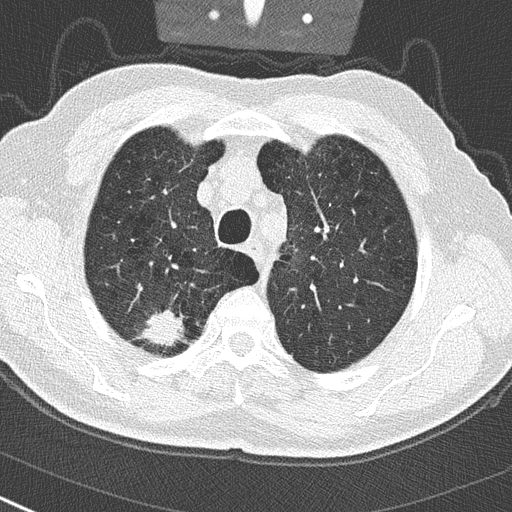
Chest CT (low-dose screening protocol), one axial image; first (baseline) screen; lung window (W 1500 / L -600 HU). Male participant, aged 65 years at enrolment.
Lesion marked by an expert reader, bounding box <134,302,189,354> (left, top, right, bottom; pixels). Reader record for this screening exam (exam-level; its link to the box is not recorded): non-calcified nodule or mass ≥4 mm, right upper lobe, 24 × 19 mm, spiculated (stellate) margins, soft tissue attenuation. Official screen result: positive, change unspecified: nodule(s) >= 4 mm or enlarging nodule(s), mass(es), or other non-specific abnormalities suspicious for lung cancer. Participant outcome: lung cancer diagnosed 32 days after this screen — non-small cell carcinoma, right upper lobe, poorly differentiated (G3), stage IA (AJCC 6th edition), 29 mm at pathology.